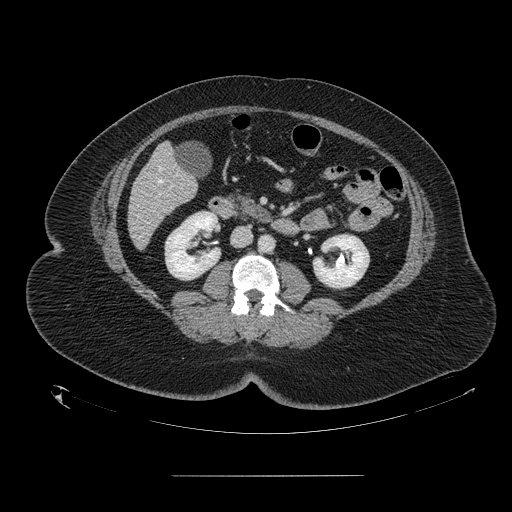
Contrast-enhanced abdominal CT, one axial slice; position 49 of 164 along the scan axis; intravenous contrast given; soft-tissue window (W 400 / L 40 HU); 512 × 512 image matrix, field of view 495 × 495 mm. Female patient, age 52 years. From the clinical record (not read from this slice): diagnosis: colorectal cancer liver metastases, imaged before liver resection; multiple liver metastases: yes; largest metastasis: 3.5 cm; disease in both lobes: no.
Outlined on this slice (expert manual segmentation):
- hepatic veins: bounding box (x1, y1, x2, y2) in pixels: (158, 167, 162, 183)
- liver: (128, 145, 197, 248)